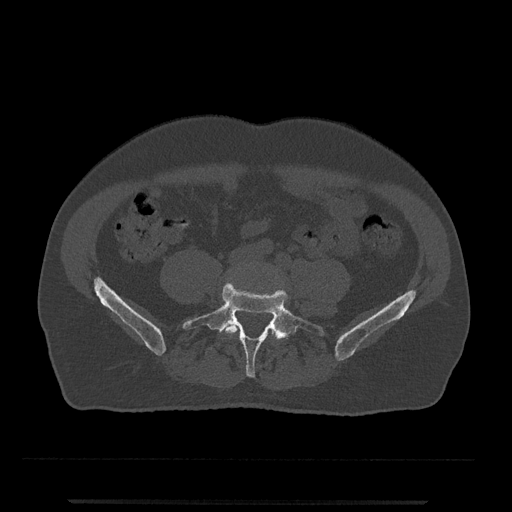
CT including the spine, one axial slice; position 86 of 797 along the scan axis; reconstruction kernel Br40s/3; 120 kVp; bone window (W 1800 / L 400 HU); 0.5 mm slice thickness; 512 × 512 image matrix, field of view 419 × 419 mm. Patient: male, 63 years. From the clinical record (not read from this slice): primary cancer: prostate.
Annotated regions visible in this slice (semi-automatic segmentation, software-assisted and operator-edited):
- L4 vertebra: bounding box <224,320,276,335> (left, top, right, bottom; pixels)
- L5 vertebra: <182,282,325,377>